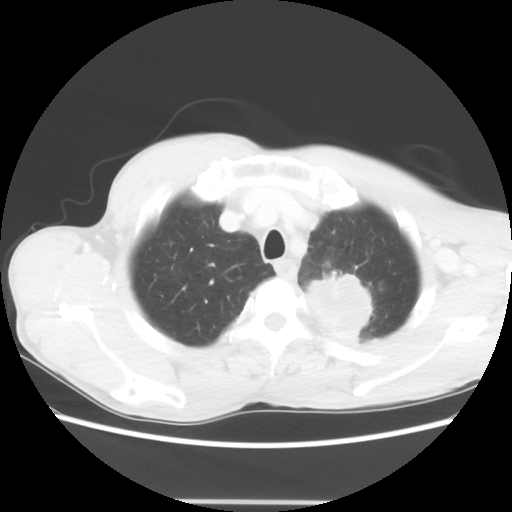
Chest CT, one axial slice. Position 55 of 62 along the scan axis. Reconstruction kernel STANDARD. 100 kVp. Lung window (W 1500 / L -600 HU). 512 × 512 image matrix, field of view 360 × 360 mm. Patient: male, 61 years. Case-level facts recorded for this patient, not image findings: clinical TNM (as recorded): T3 N1 M1.
Outlined on this slice (bounding box drawn by a radiologist):
- lung tumour (recorded histology: adenocarcinoma): bounding box [x1, y1, x2, y2] px = [306, 265, 378, 345]